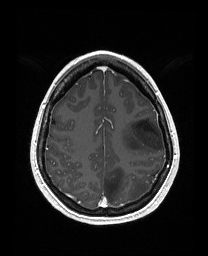
Brain MRI from a brain-tumour surgery series, one axial slice; slice 120 of 176 in the series (ordered by position); T1-weighted post-contrast; 1 mm slice thickness; 208 × 256 image matrix, field of view 203 × 250 mm. From the clinical record (not read from this slice): histopathology: Astrocytoma; WHO grade: 3; IDH mutation: yes; tumour location: Left Frontal.
Outlined on this slice (expert manual segmentation):
- tumour: bounding box (x1, y1, x2, y2) in pixels: (121, 116, 164, 153)